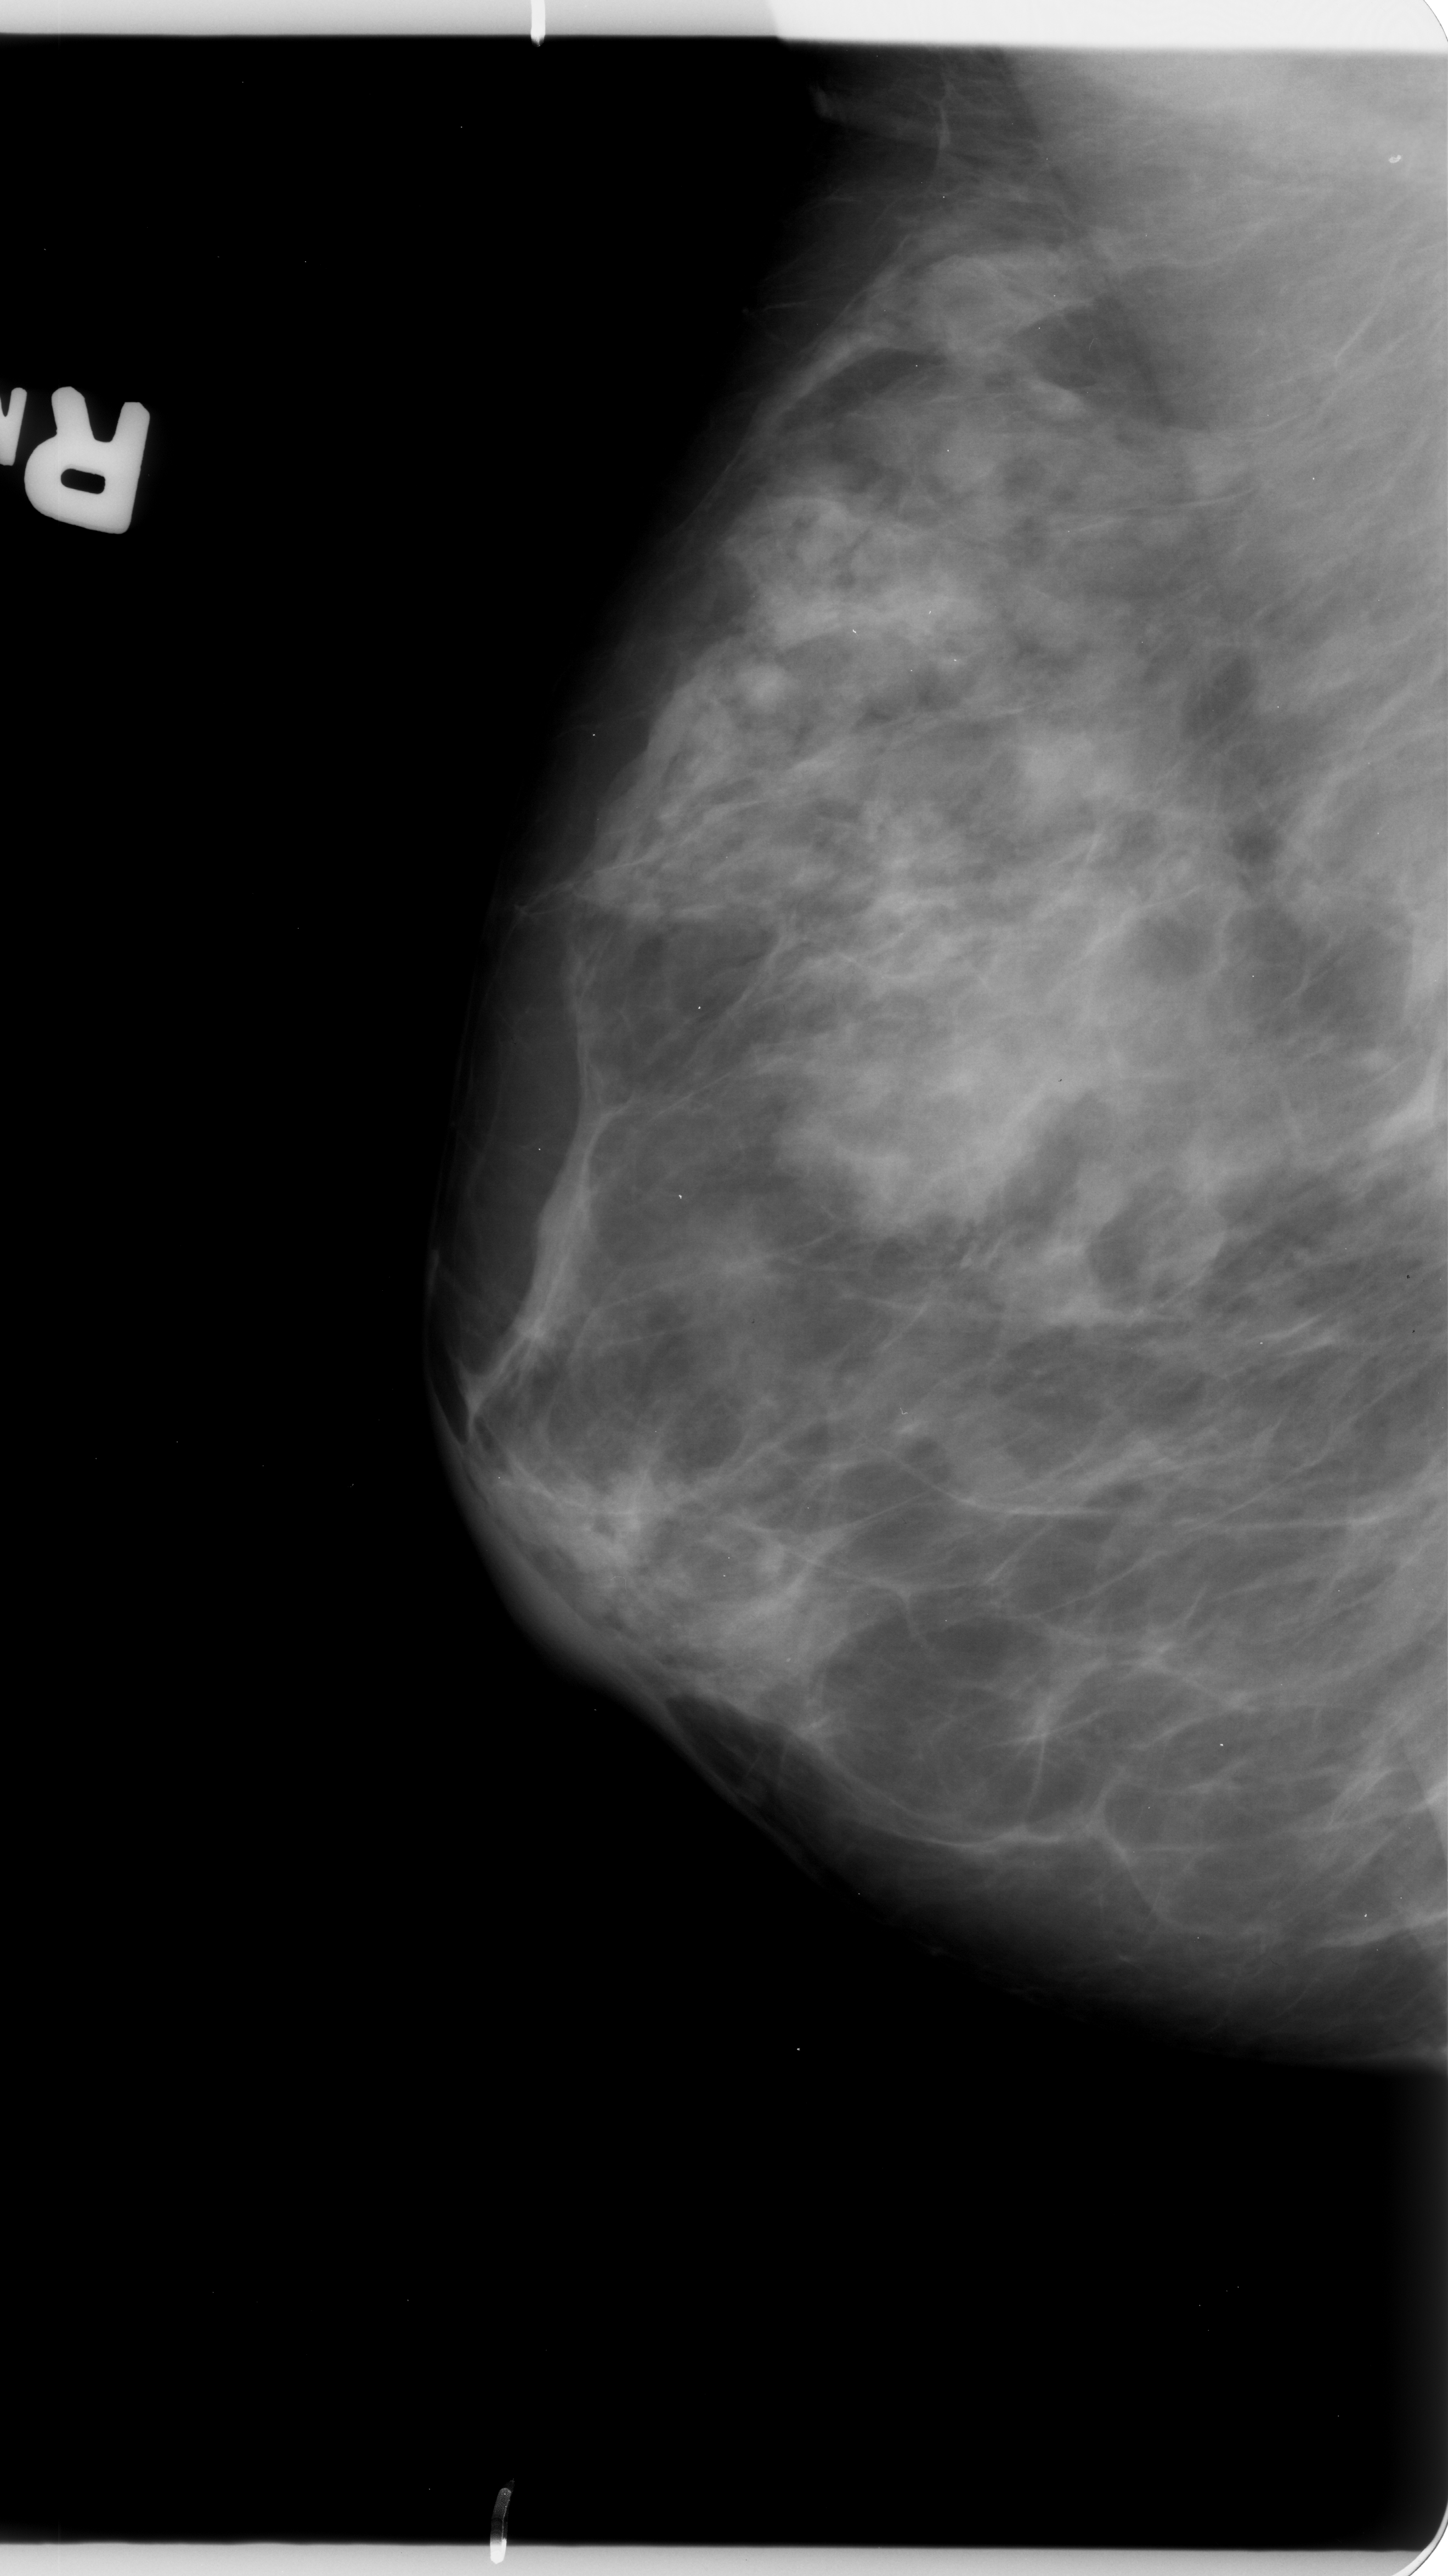
Scanned film-screen mammogram; right breast; mediolateral oblique (MLO) view; BI-RADS breast density category 3 (scale 1–4); 1448 × 2576 image matrix.
Expert-marked regions of interest on this image (one box per marked abnormality):
- mass, shape irregular / focal asymmetric density, margins ill defined; BI-RADS assessment category 3; pathology (as recorded): benign: bounding box (x1, y1, x2, y2) in pixels: (765, 954, 1109, 1237)